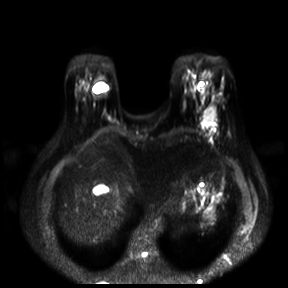
Breast MRI, one axial slice; slice 5 of 30 in the series (ordered by position); diffusion-weighted series; image 2 of 4 stored at this slice position (different b-values; order by instance number); 3 T; 4 mm slice thickness; 288 × 288 image matrix. Female patient.
Outlined on this slice (manually delineated by an expert):
- tumour on diffusion-weighted imaging: bounding box (x1, y1, x2, y2) in pixels: (204, 107, 216, 125)